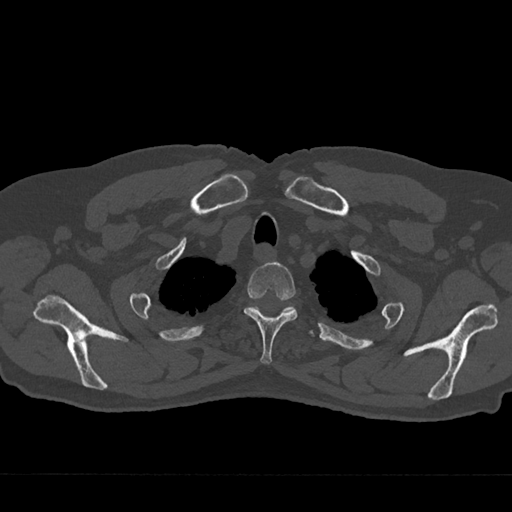
CT including the spine, one axial slice; slice 605 of 797 in the series (ordered by position); reconstruction kernel Br40s/3; 120 kVp; bone window (W 1800 / L 400 HU); 0.5 mm slice thickness; 512 × 512 image matrix. Patient: male, 75 years. From the clinical record (not read from this slice): primary cancer: renal; vertebrae with lytic lesions (as recorded): T4.
Structures marked on this image (semi-automatic segmentation, software-assisted and operator-edited):
- T2 vertebra: bounding box (x1, y1, x2, y2) in pixels: (244, 262, 297, 364)
- T3 vertebra: (253, 306, 314, 337)